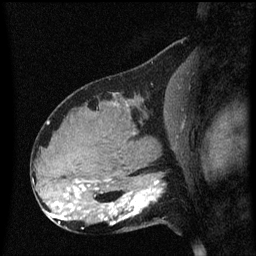
Breast MRI (dynamic contrast-enhanced), one sagittal slice; position 30 of 60 along the scan axis; dynamic contrast-enhanced series, image 2 of 3 at this slice position (ordered by acquisition); 1.5 T; TE 4.2 ms, TR 8.4 ms; 256 × 256 image matrix, field of view 200 × 200 mm. Female patient, age 31 years. Case-level facts recorded for this patient, not image findings: setting: breast cancer imaged before/during neoadjuvant chemotherapy; receptor status: HR-positive, HER2-negative.
Annotated regions visible in this slice (semi-automatically segmented with operator editing):
- analysis volume of interest (the breast-tissue region the enhancement analysis was run in; not a lesion): bounding box <102,166,170,229> (left, top, right, bottom; pixels)
- tumour enhancement mask (voxels above the 70 % enhancement threshold inside the analysis volume of interest): <105,180,160,223>